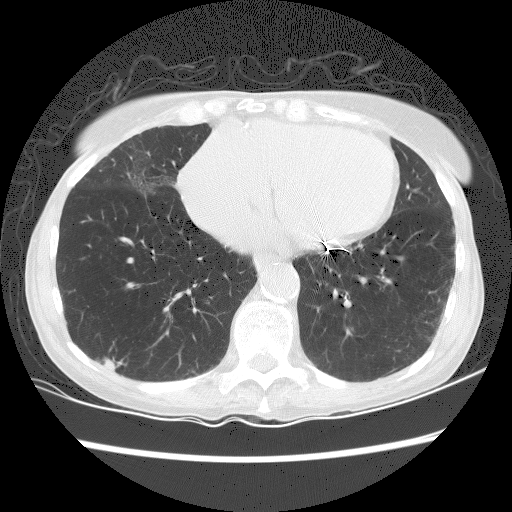
Low-dose screening chest CT, one axial slice; lung window (W 1500 / L -600 HU); 2.5 mm slice thickness; 512 × 512 image matrix.
Structures marked on this image (manually delineated by an expert):
- lesion 1 (tumor, lower lobe of right lung): bounding box <103,357,126,370> (left, top, right, bottom; pixels)